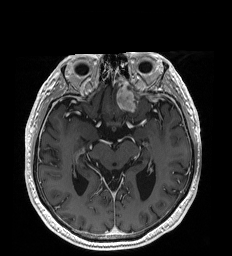
Brain MRI from a brain-tumour surgery series, one axial slice. Slice 114 of 192 in the series (ordered by position). T1-weighted post-contrast. 232 × 256 image matrix. From the clinical record (not read from this slice): histopathology: Glioblastoma; WHO grade: 4; IDH mutation: no.
Structures marked on this image (outlined manually by an expert reader):
- tumour: box from (x=116, y=88) to (x=136, y=112) px